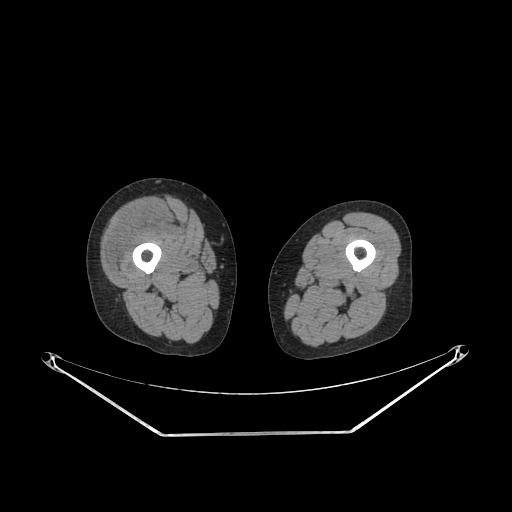
CT of an extremity soft-tissue mass (from a PET/CT study), one axial slice. Slice 223 of 311 in the series (ordered by position). Soft-tissue window (W 400 / L 40 HU). 3.75 mm slice thickness. 512 × 512 image matrix, field of view 500 × 500 mm. Female patient. From the clinical record (not read from this slice): histological type: pleiomorphic undifferentiated sarcoma; grade: high; site of the primary tumour: right quadricep.
Outlined on this slice (expert contour drawn on MRI and transferred to this co-registered scan by the dataset authors):
- tumour plus oedema (research contour): bounding box [x1, y1, x2, y2] px = [107, 203, 163, 273]